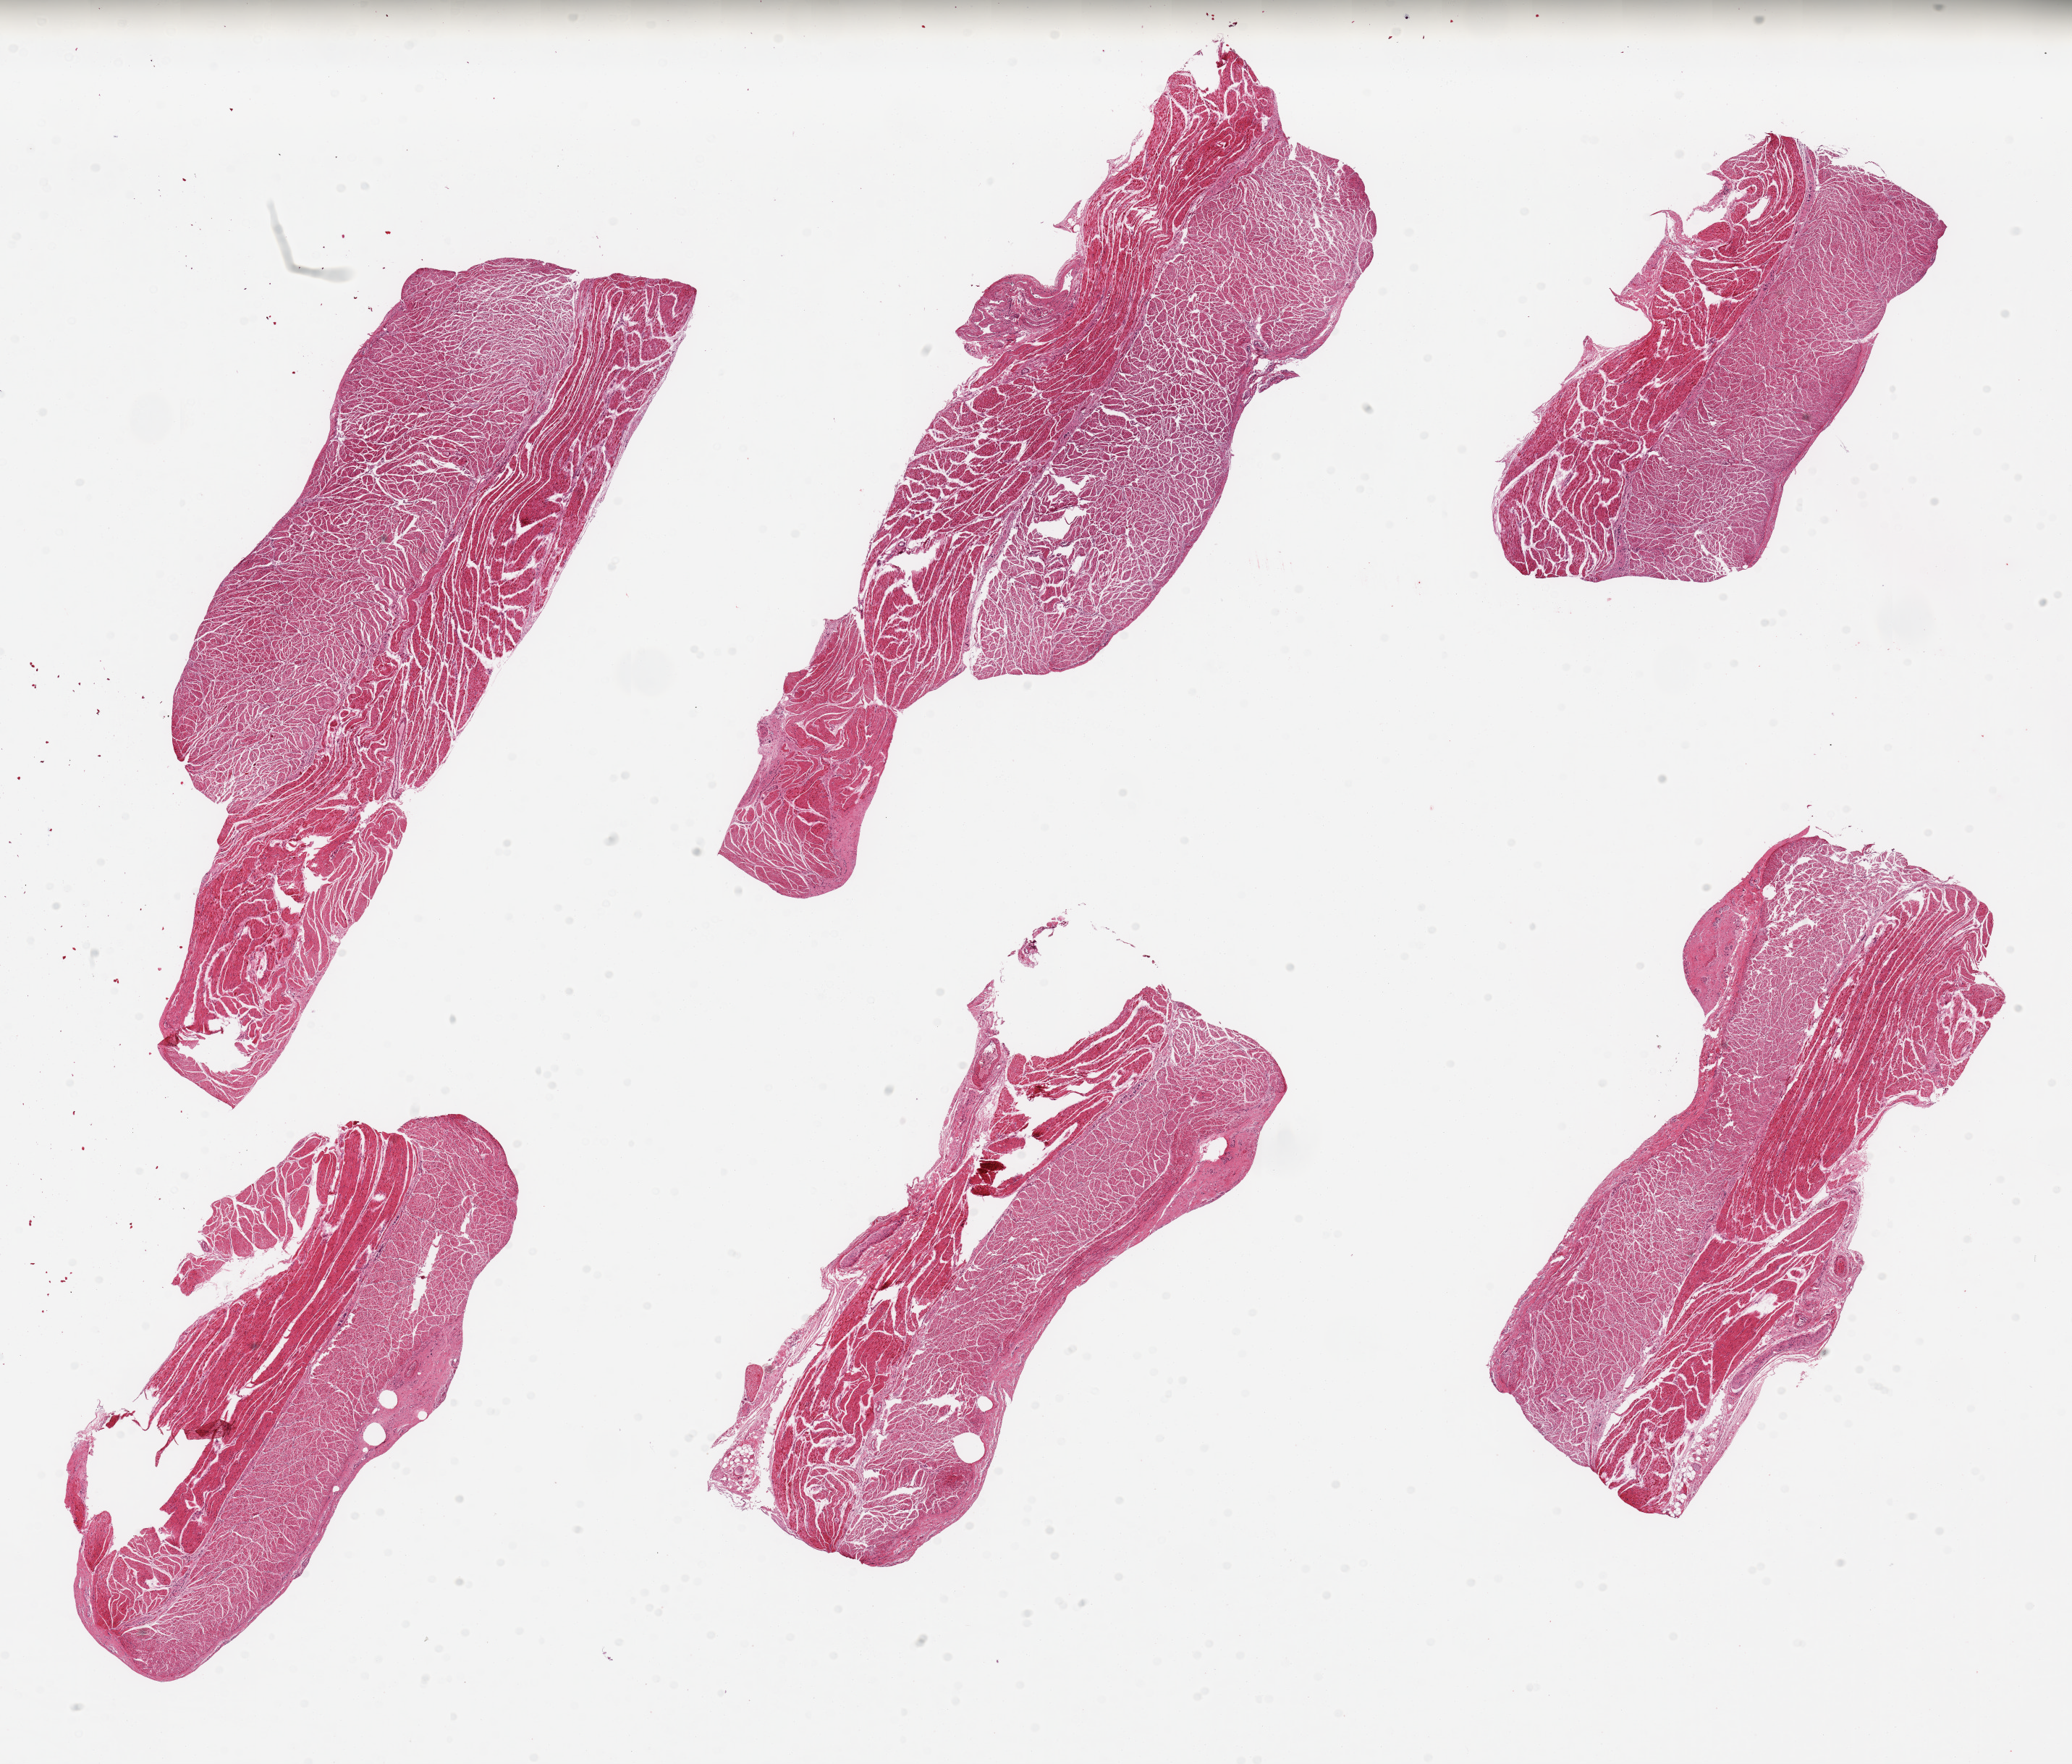
Whole-slide image, hematoxylin and eosin (H&E) stain — whole scanned area (about 22.6 x 19.3 mm, from a 20x scan) shown as a low-resolution overview; PAXgene-fixed paraffin-embedded (PFPE) section; target tissue: esophageal muscle; donor tissue sample. Donor sex: male.
Reviewer comment on this tissue sample: 6 pieces; well dissected but not well preserved.